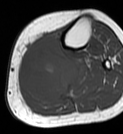
MRI of an extremity soft-tissue mass, one axial slice; position 31 of 68 along the scan axis; MR volume resampled by the dataset authors to the PET/CT grid (not the native acquisition matrix); 123 × 134 image matrix. Female patient. Case-level facts recorded for this patient, not image findings: histological type: extraskeletal high grade osteogenic sarcoma; grade: high; site of the primary tumour: left calf.
Structures marked on this image (expert contour drawn on MRI and transferred to this co-registered scan by the dataset authors):
- gross tumour volume (mass): box from (x=20, y=36) to (x=75, y=102) px